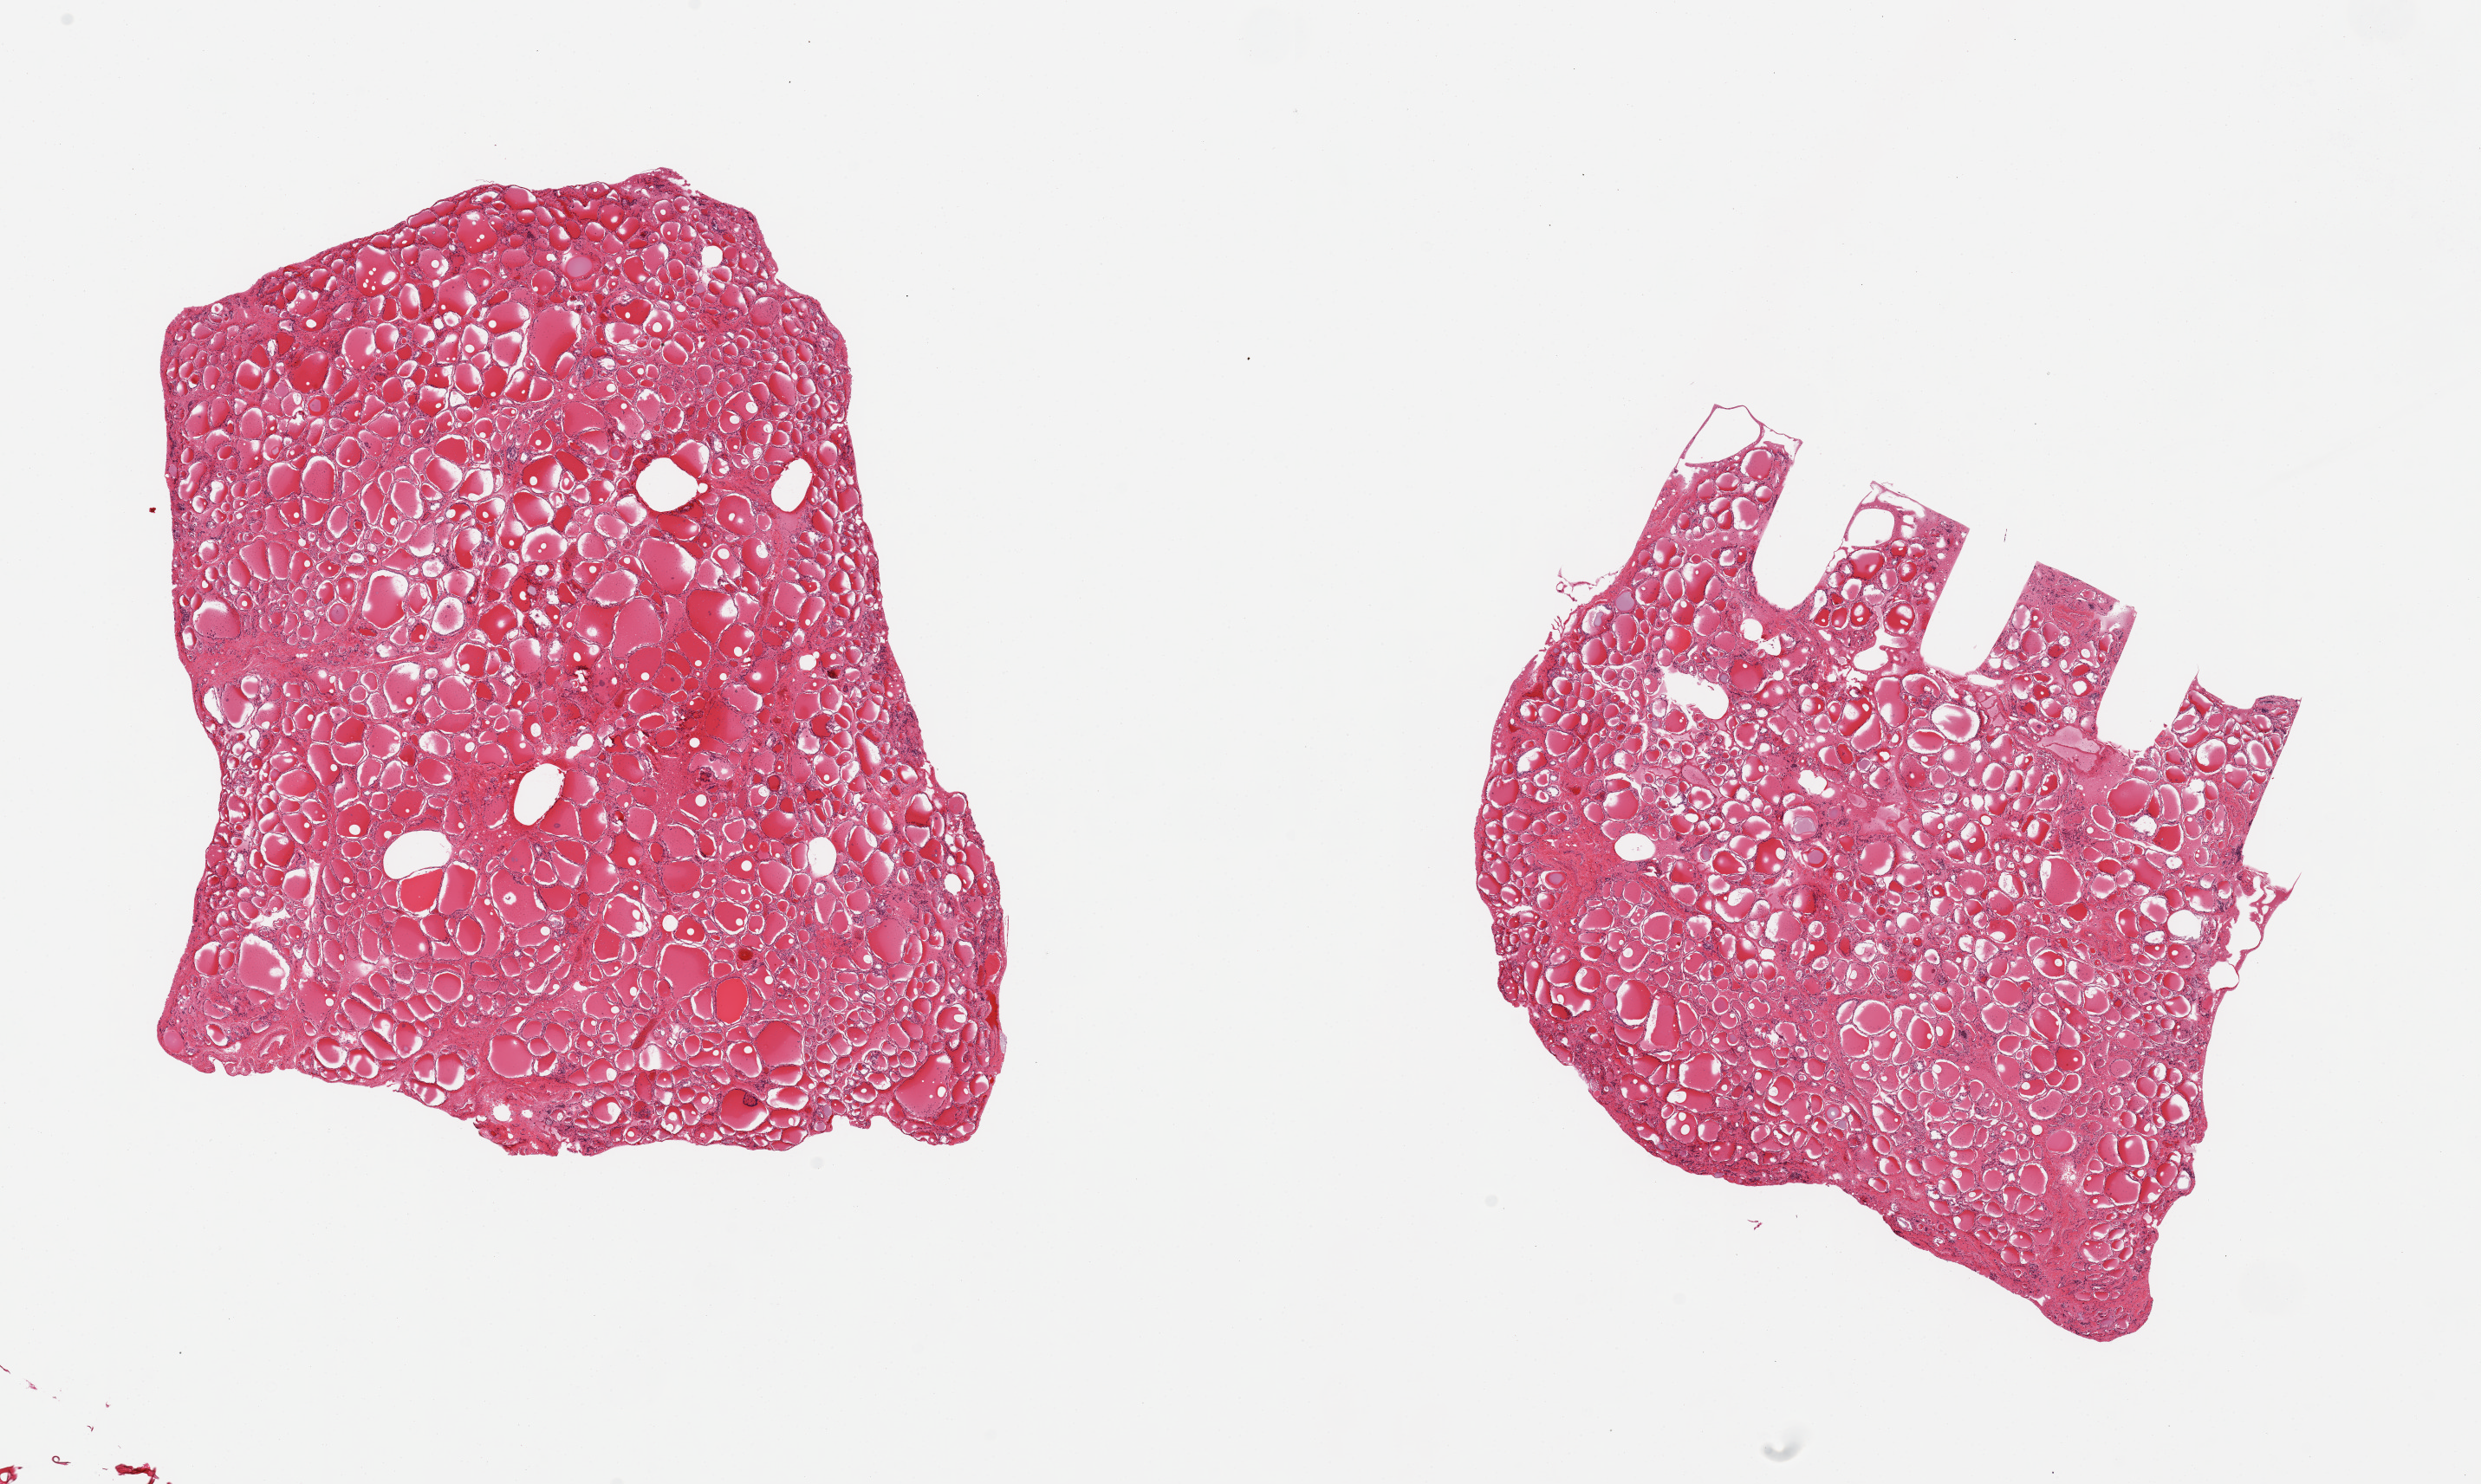
H&E whole-slide image, brightfield, whole scanned area (about 22.6 x 13.5 mm, slide scanned at 20x) shown as a low-resolution overview; PAXgene-fixed paraffin-embedded (PFPE) section; sampled site (target tissue): thyroid; donor tissue sample. Donor: male.
• pathologist's review note for this sample: 2 pieces; some interstitial fibrosis